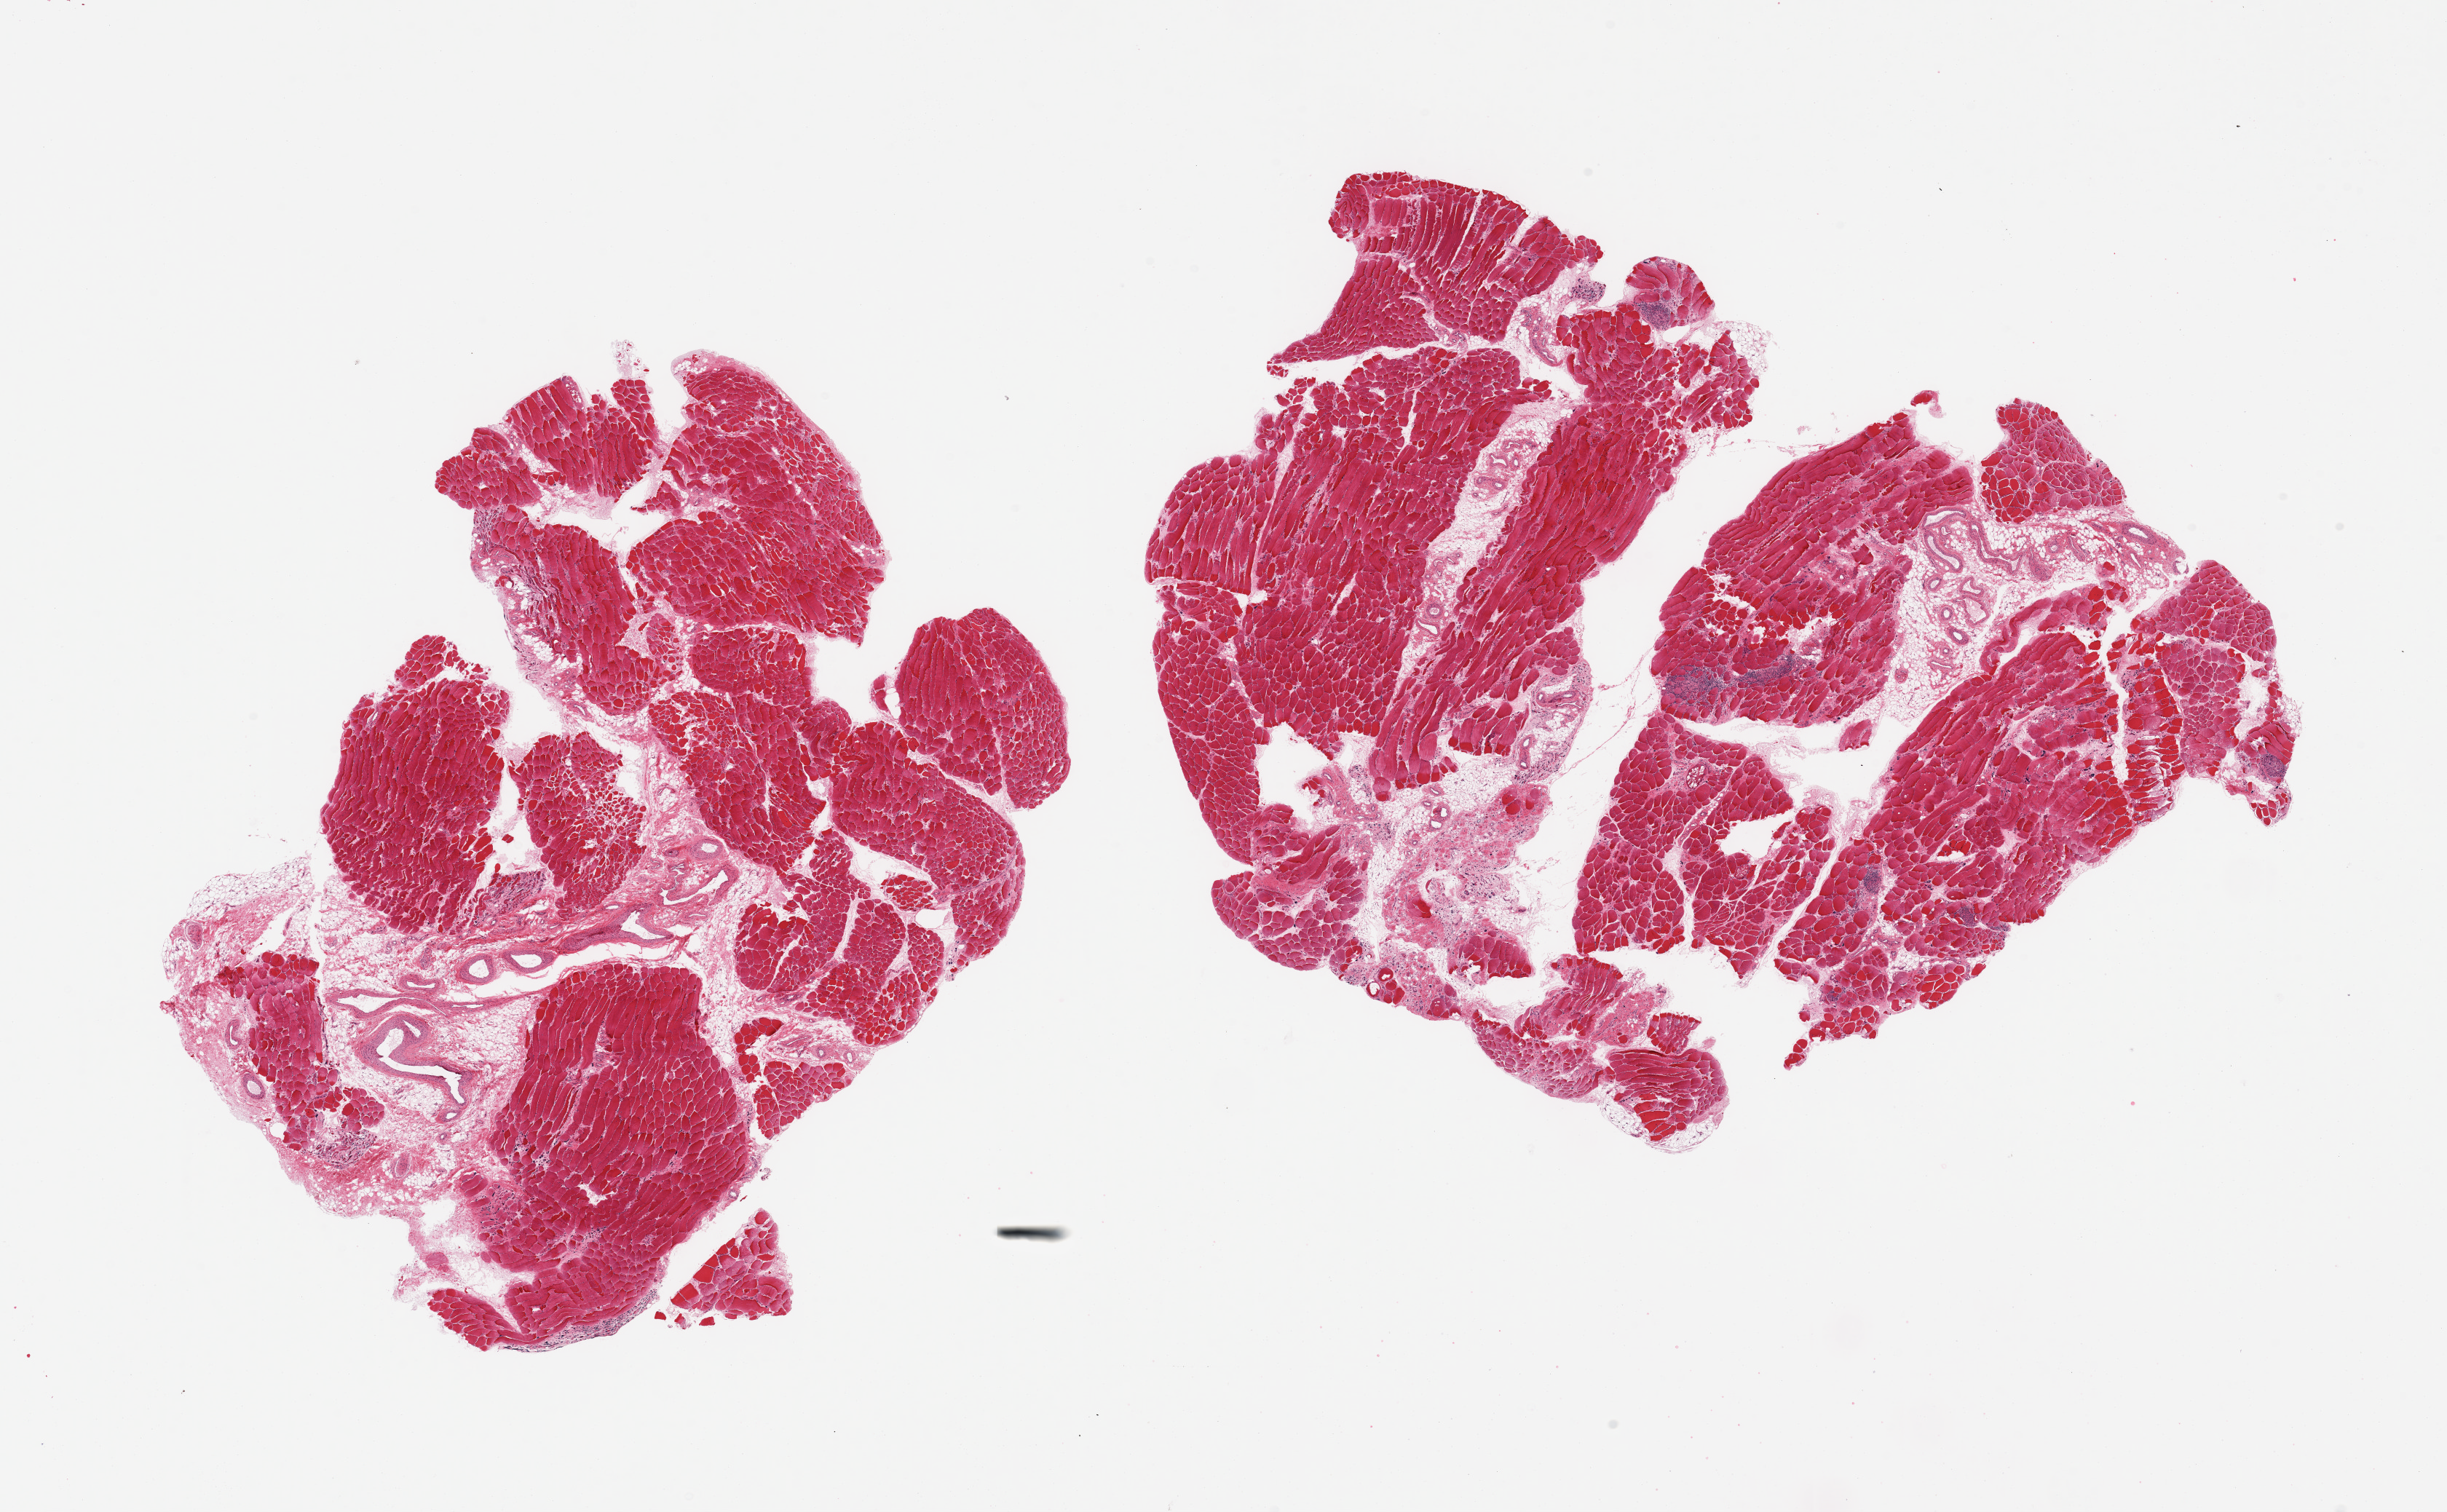
Hematoxylin and eosin (H&E) whole-slide image — whole scanned area (about 26.6 x 16.4 mm) shown as a low-resolution overview, PAXgene-fixed, paraffin-embedded tissue, section of skeletal muscle (target tissue), donor tissue sample.
Reviewer comment on this tissue sample: 2 pieces; foci of atrophy some with lymphoid aggregates; 10 & 20% internal fibrovascular fatty content.